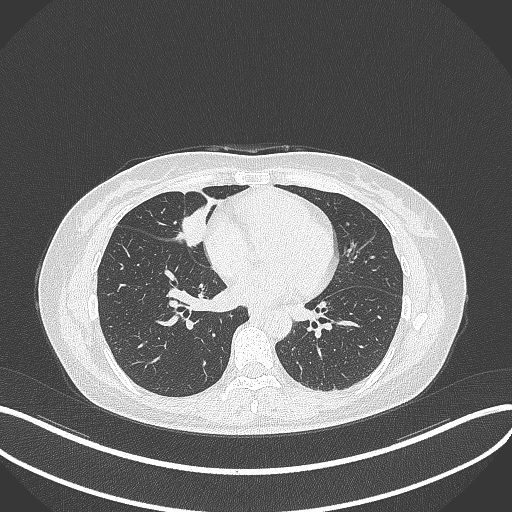
Chest CT, one axial slice. Position 119 of 284 along the scan axis. Lung window (W 1500 / L -600 HU). 1 mm slice thickness. 512 × 512 image matrix, field of view 400 × 400 mm. Female patient, age 43 years. Case-level facts recorded for this patient, not image findings: clinical TNM (as recorded): T1c N3 M1; histopathological grade: G1.
Annotated regions visible in this slice (rectangle marked by the reading radiologist):
- lung tumour (recorded histology: adenocarcinoma): bounding box [x1, y1, x2, y2] px = [178, 200, 208, 248]